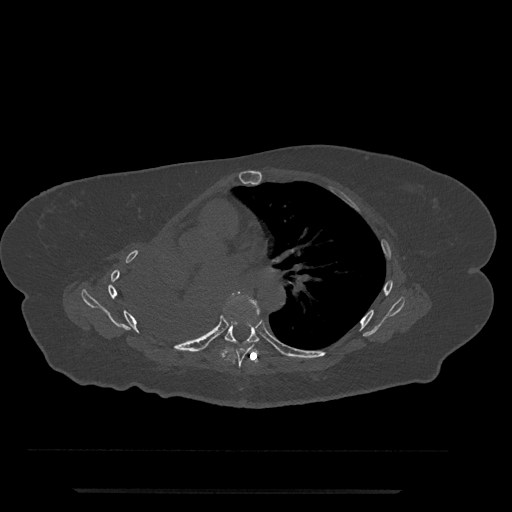
CT including the spine, one axial slice; position 469 of 797 along the scan axis; bone window (W 1800 / L 400 HU); 0.5 mm slice thickness; 512 × 512 image matrix, field of view 440 × 440 mm. Patient: female, 51 years. Case-level facts recorded for this patient, not image findings: primary cancer: neuro; vertebrae with lytic lesions (as recorded): T8.
Structures marked on this image (semi-automatic segmentation, software-assisted and operator-edited):
- T6 vertebra: bounding box [x1, y1, x2, y2] px = [223, 293, 260, 368]
- T7 vertebra: [225, 318, 259, 345]